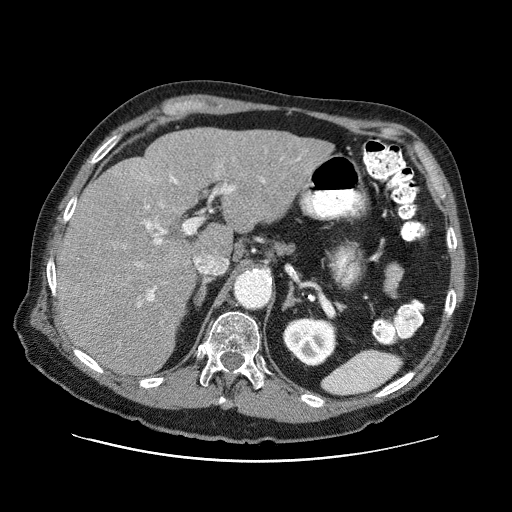
Contrast-enhanced abdominal CT (liver protocol), one axial slice. Position 46 of 87 along the scan axis. One of 3 acquisitions stored at this slice position. Soft-tissue window (W 400 / L 40 HU). 512 × 512 image matrix. From the clinical record (not read from this slice): diagnosis: hepatocellular carcinoma (patient treated with transarterial chemoembolisation; whether this scan precedes or follows treatment is not stated here); TNM stage (as recorded): Stage-IIIA; Child-Pugh class: A; tumour differentiation: well differentiated; tumour nodularity: multinodular.
Outlined on this slice (semi-automatically segmented with operator editing):
- liver parenchyma outside the tumour (the mass and vessels are separate outlines, so this box may not span the whole liver): bounding box <58,128,332,374> (left, top, right, bottom; pixels)
- liver vessels: <137,158,300,306>